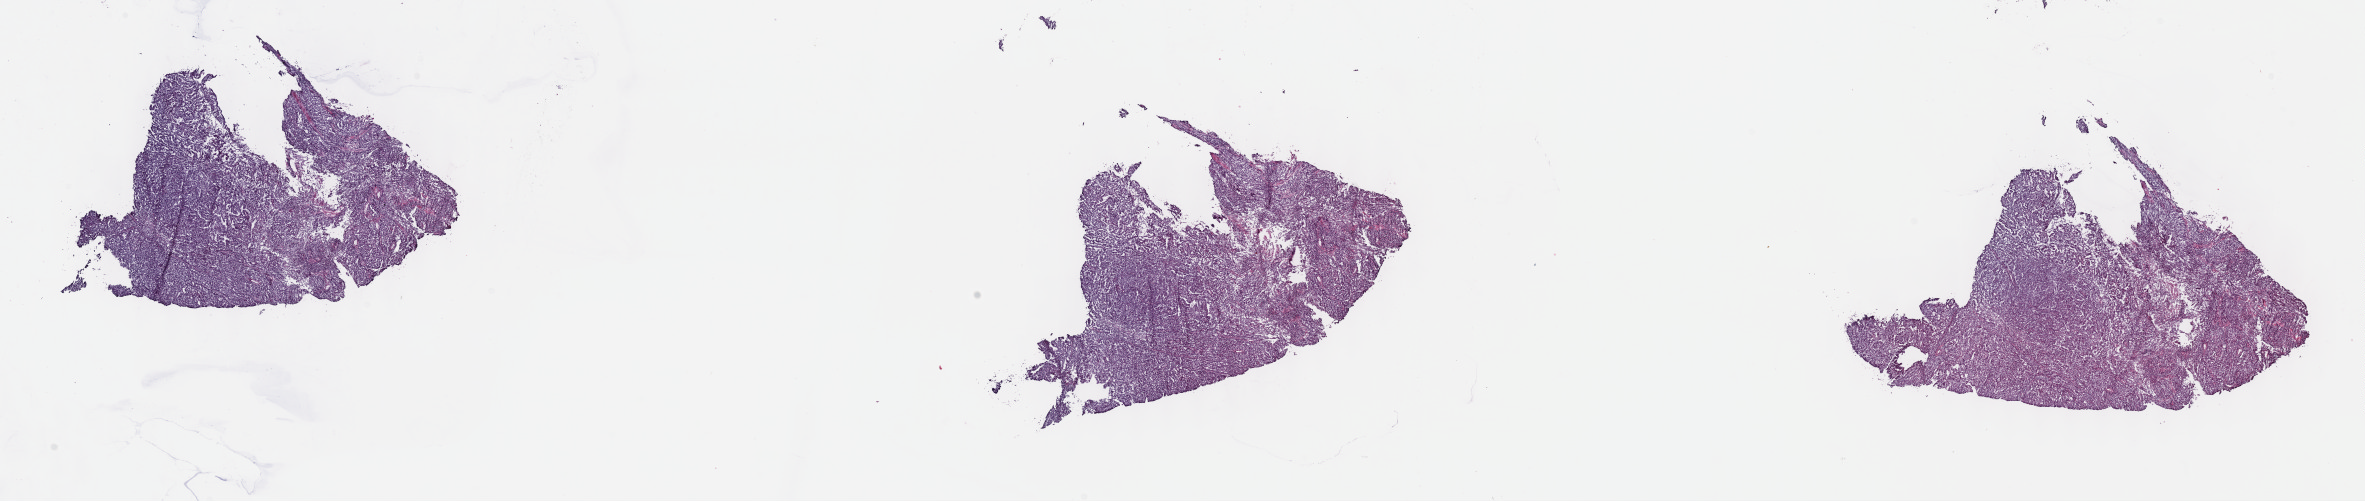
H&E whole-slide image, whole scanned area (about 38.3 x 8.1 mm) shown as a low-resolution overview, frozen section from the top of the tissue portion, primary tumour sample from the kidney. Male, age 62 years at initial diagnosis. Composition of this section per pathologist review: tumour cells 80%, tumour nuclei 80%.
Histologic diagnosis: Papillary adenocarcinoma, NOS.